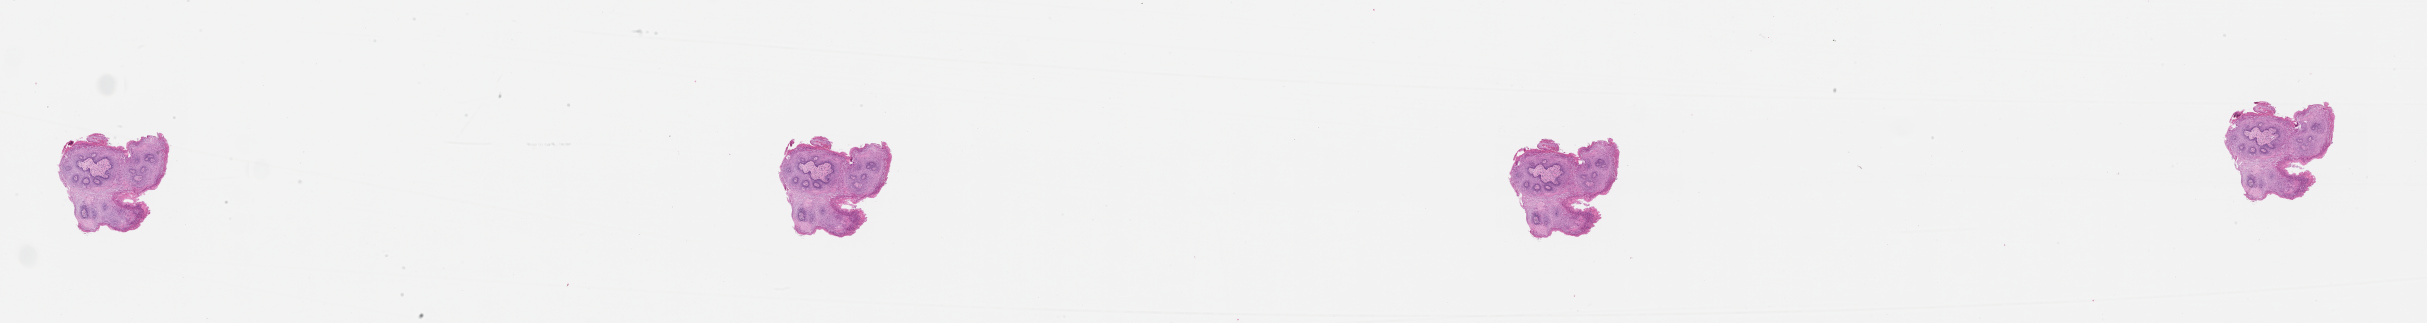
Whole-slide histology image, H&E, a low-resolution overview of the entire scanned area, about 39.1 x 5.2 mm; head and neck, tissue type not recorded. Male, 63 y/o.
Patient diagnosis: Squamous cell carcinoma, NOS (floor of mouth, NOS).